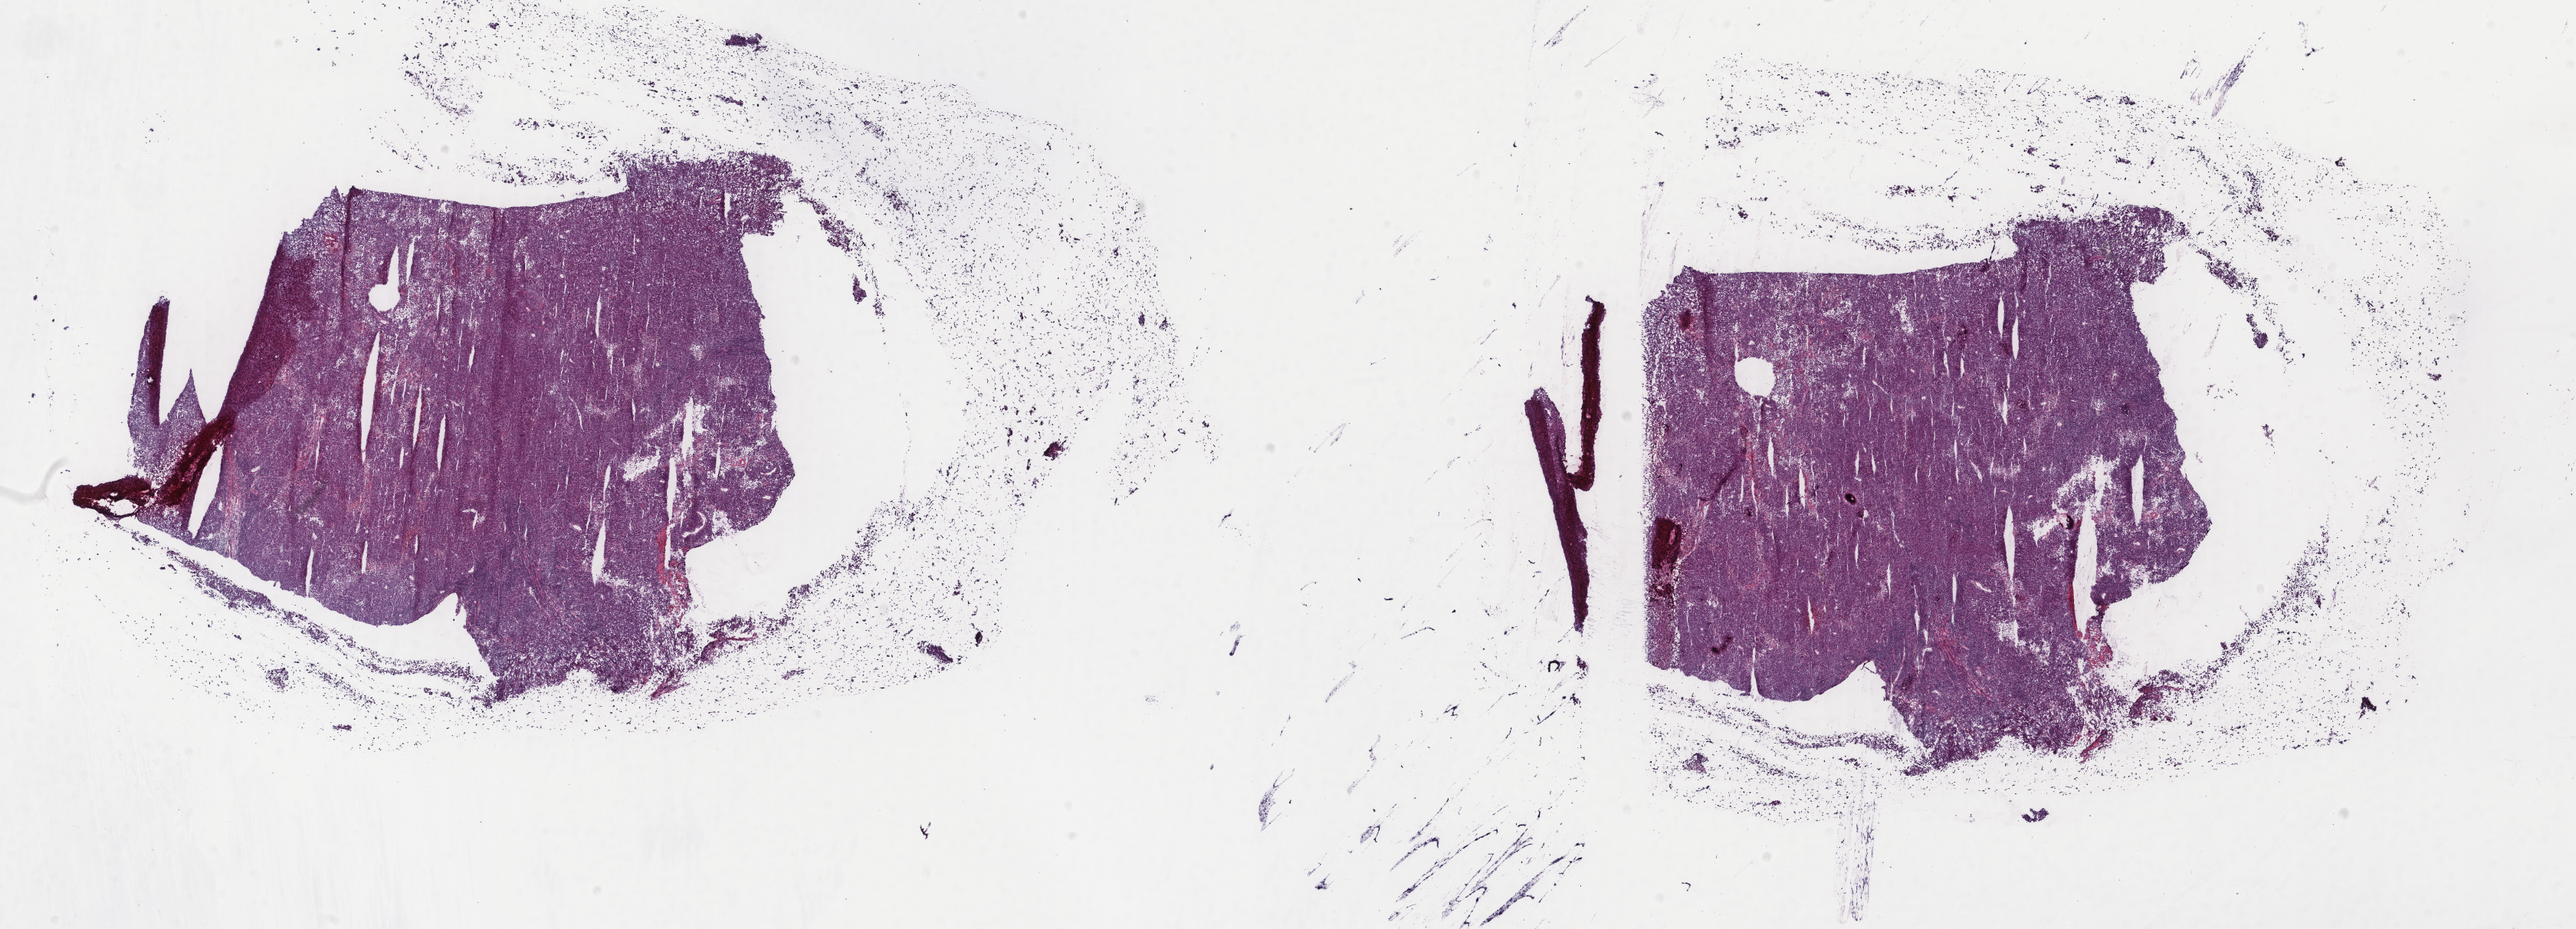
Whole-slide histology image, H&E-stained, shown as a low-resolution overview of the whole scanned area (about 26.7 x 9.6 mm); frozen section from the top of the tissue portion; metastatic tumour sample, sampled site: lymph nodes of inguinal region or leg. Female patient; age at initial diagnosis 82 years. Pathologist review of this section (percent, as recorded): tumour cells 90%, tumour nuclei 90%.
This section: metastatic tumour tissue. Patient diagnosis: Malignant melanoma, NOS.